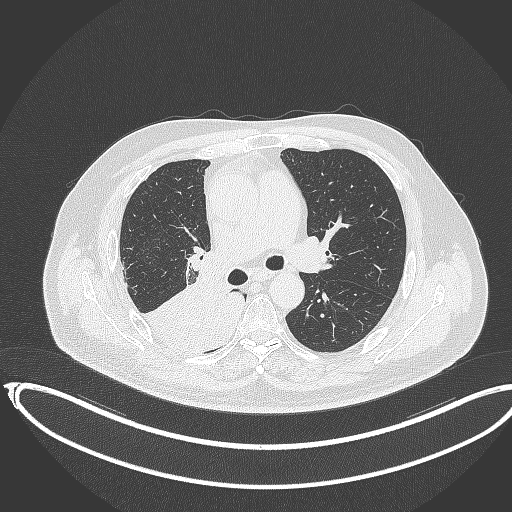
Chest CT, one axial slice. Position 214 of 403 along the scan axis. Reconstruction kernel B70f. 120 kVp. Lung window (W 1500 / L -600 HU). 512 × 512 image matrix. Male patient, age 68 years. From the clinical record (not read from this slice): clinical TNM (as recorded): T2a N0 M0.
Annotated regions visible in this slice (rectangle marked by the reading radiologist):
- lung tumour (recorded histology: adenocarcinoma): bounding box [x1, y1, x2, y2] px = [136, 283, 243, 351]